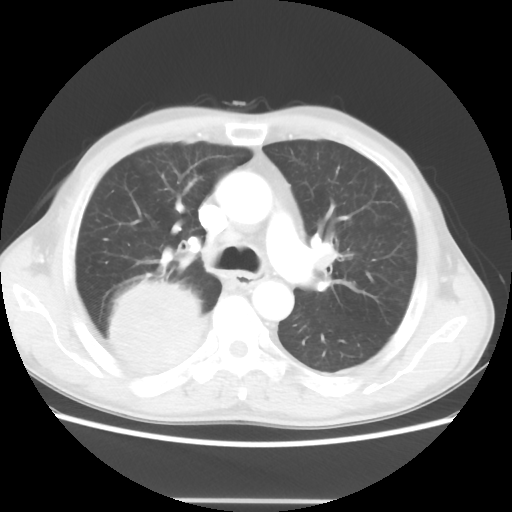
Chest CT, one axial slice; position 32 of 48 along the scan axis; lung window (W 1500 / L -600 HU); 5 mm slice thickness; 512 × 512 image matrix, field of view 361 × 361 mm. Patient: male, 66 years. Case-level facts recorded for this patient, not image findings: clinical TNM (as recorded): T4 N1 M1.
Outlined on this slice (rectangle marked by the reading radiologist):
- lung tumour (recorded histology: small cell carcinoma): bounding box [x1, y1, x2, y2] px = [103, 274, 208, 380]